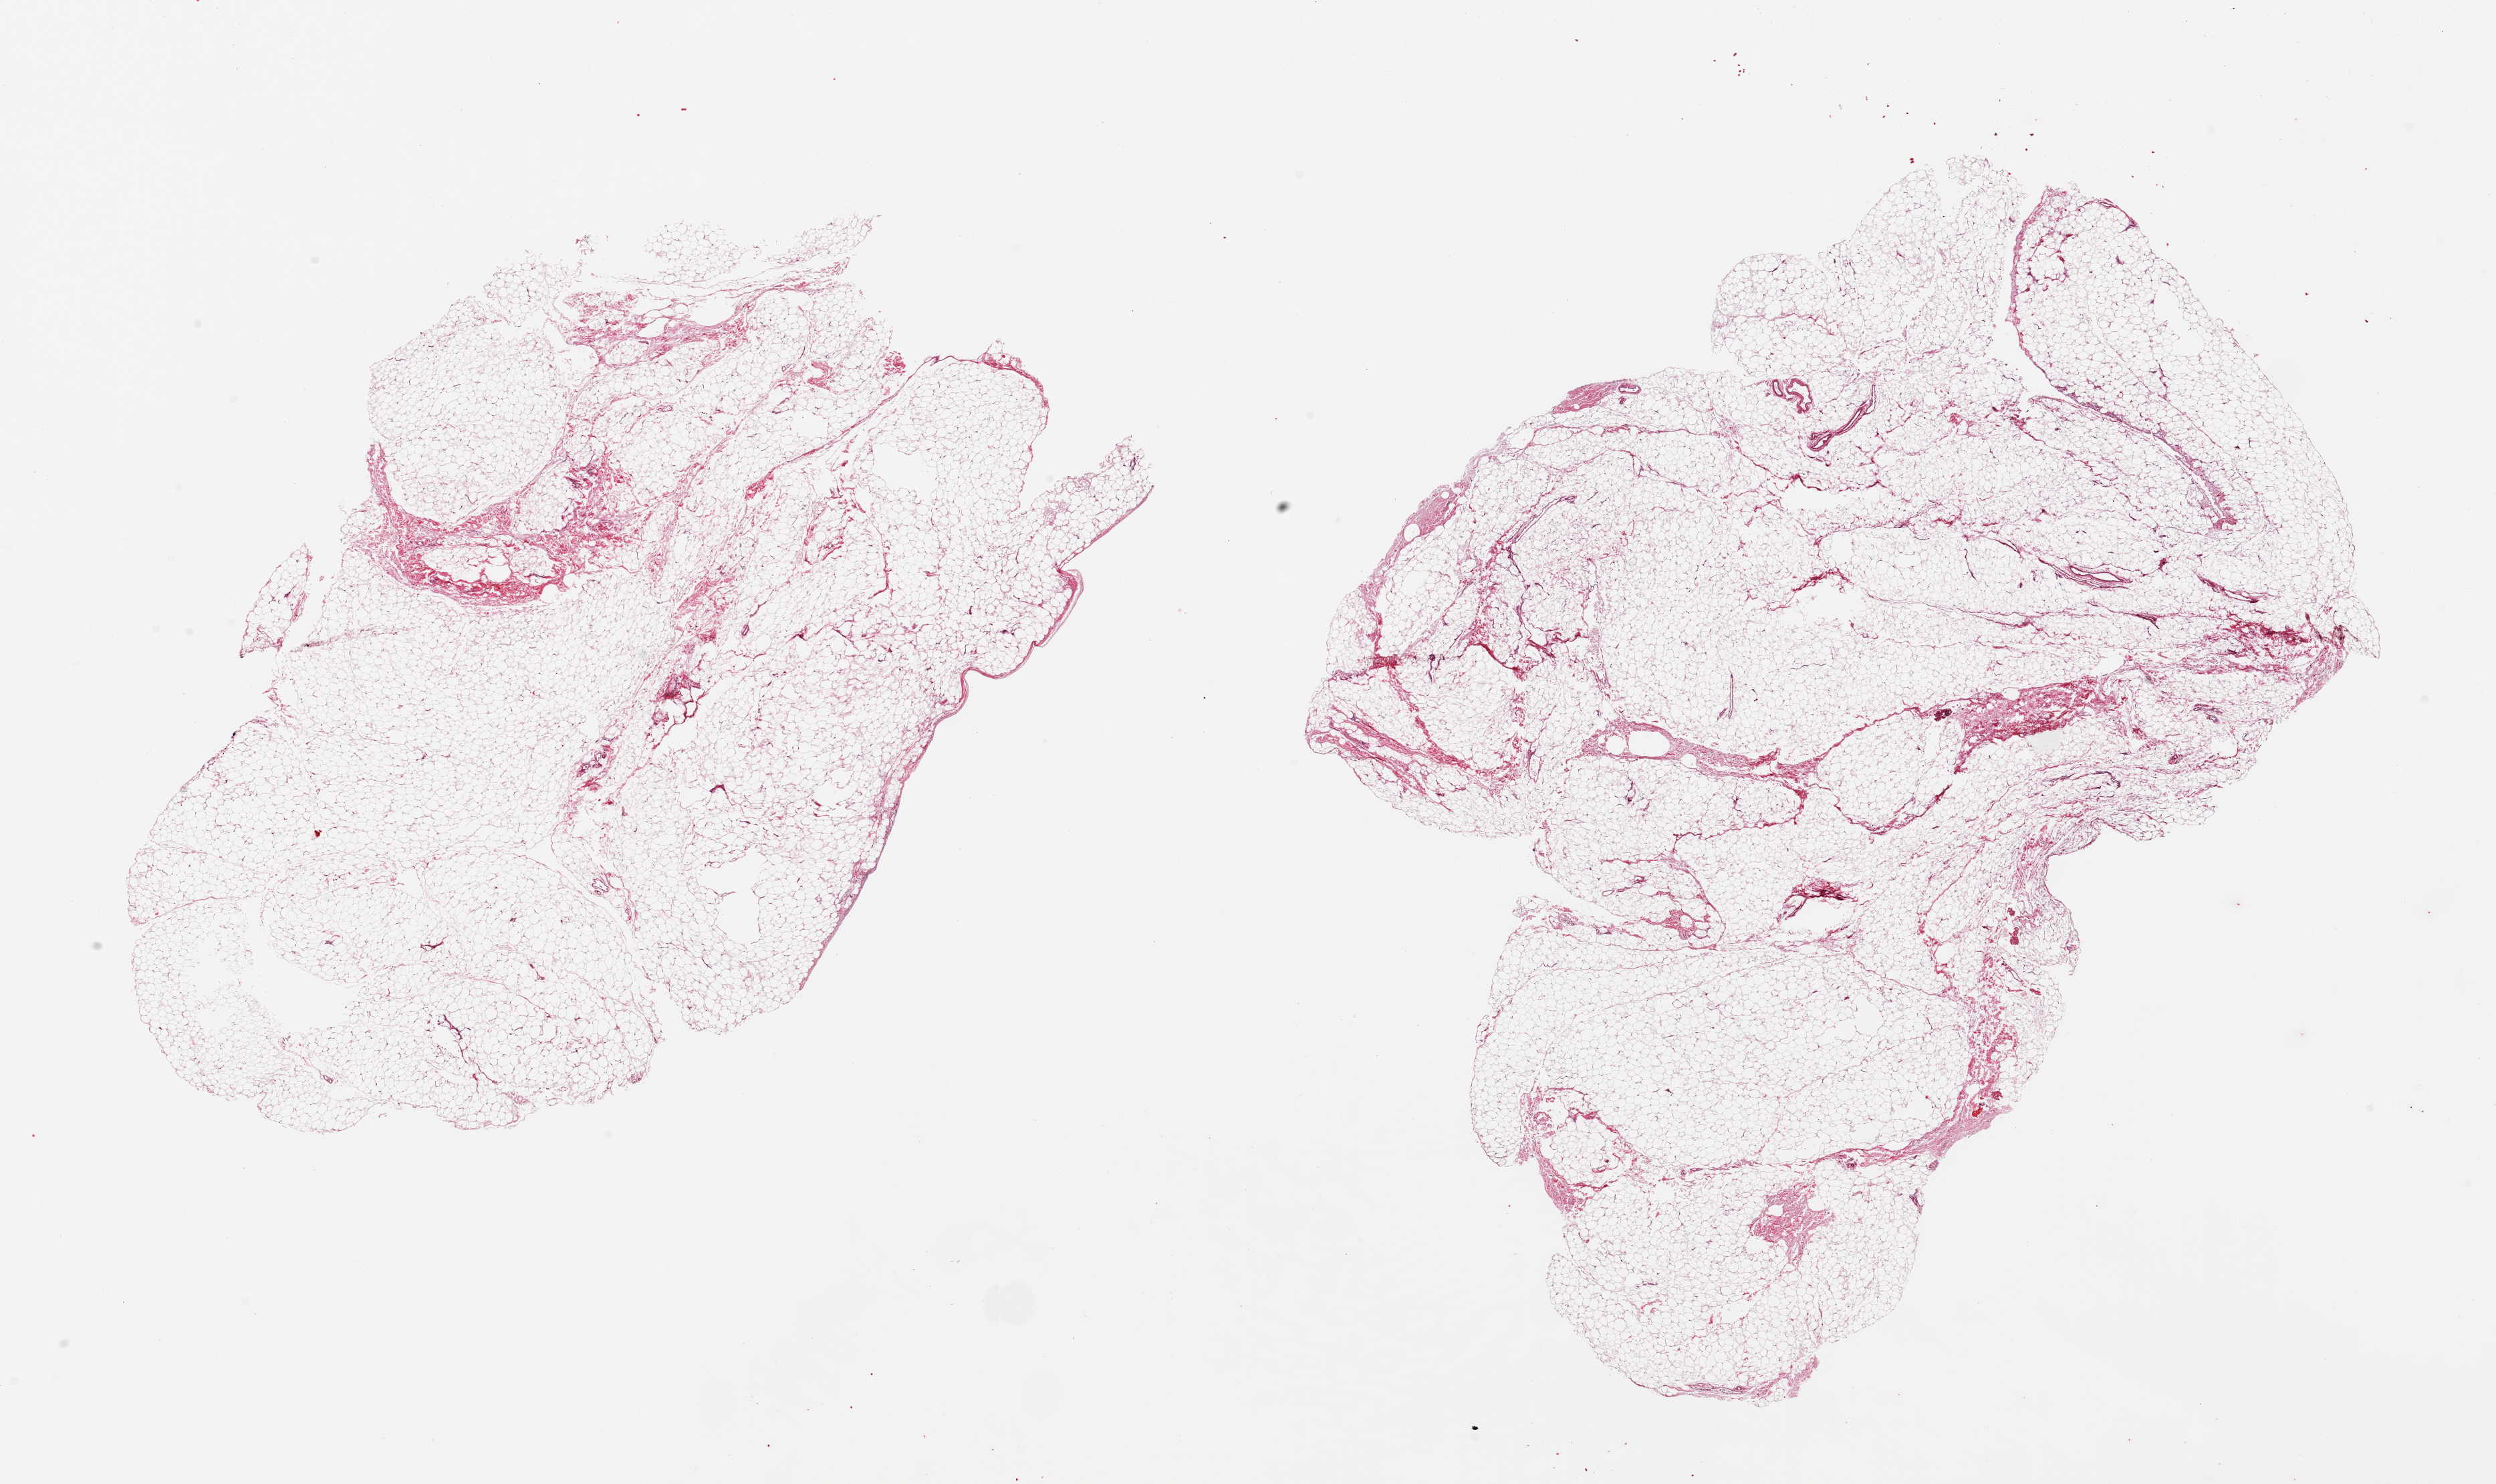
Haematoxylin and eosin whole-slide image, shown as a low-resolution overview of the whole scanned area (about 29.5 x 17.6 mm, from a 20x scan). PAXgene-fixed, paraffin-embedded tissue. Sampled site (target tissue): omentum. Tissue donor sample.
* pathologist's review note for this sample: 2 pieces